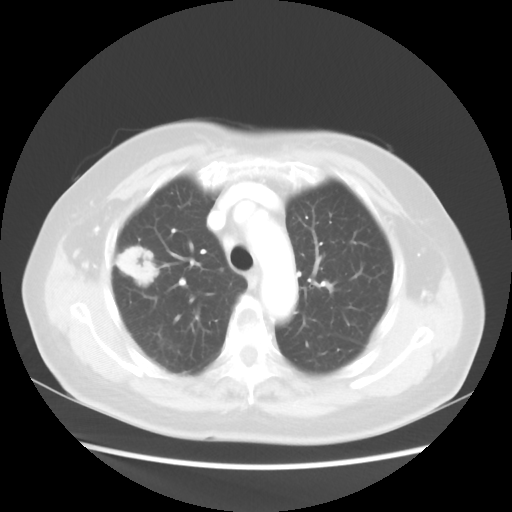
Chest CT, one axial slice; reconstruction kernel STANDARD; 100 kVp; lung window (W 1500 / L -600 HU); 5 mm slice thickness; 512 × 512 image matrix, field of view 360 × 360 mm. Patient: female, 75 years. From the clinical record (not read from this slice): clinical TNM (as recorded): T1c N0 M0.
Outlined on this slice (rectangle marked by the reading radiologist):
- lung tumour (recorded histology: adenocarcinoma): box from (x=111, y=242) to (x=160, y=293) px